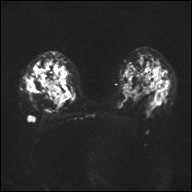
Breast MRI, one axial slice; position 25 of 32 along the scan axis; diffusion-weighted series; image 2 of 4 stored at this slice position (different b-values; order by instance number); 1.5 T; 4 mm slice thickness; 192 × 192 image matrix, field of view 360 × 360 mm. Female patient.
Structures marked on this image (outlined manually by an expert reader):
- tumour on diffusion-weighted imaging: bounding box (x1, y1, x2, y2) in pixels: (44, 79, 67, 105)